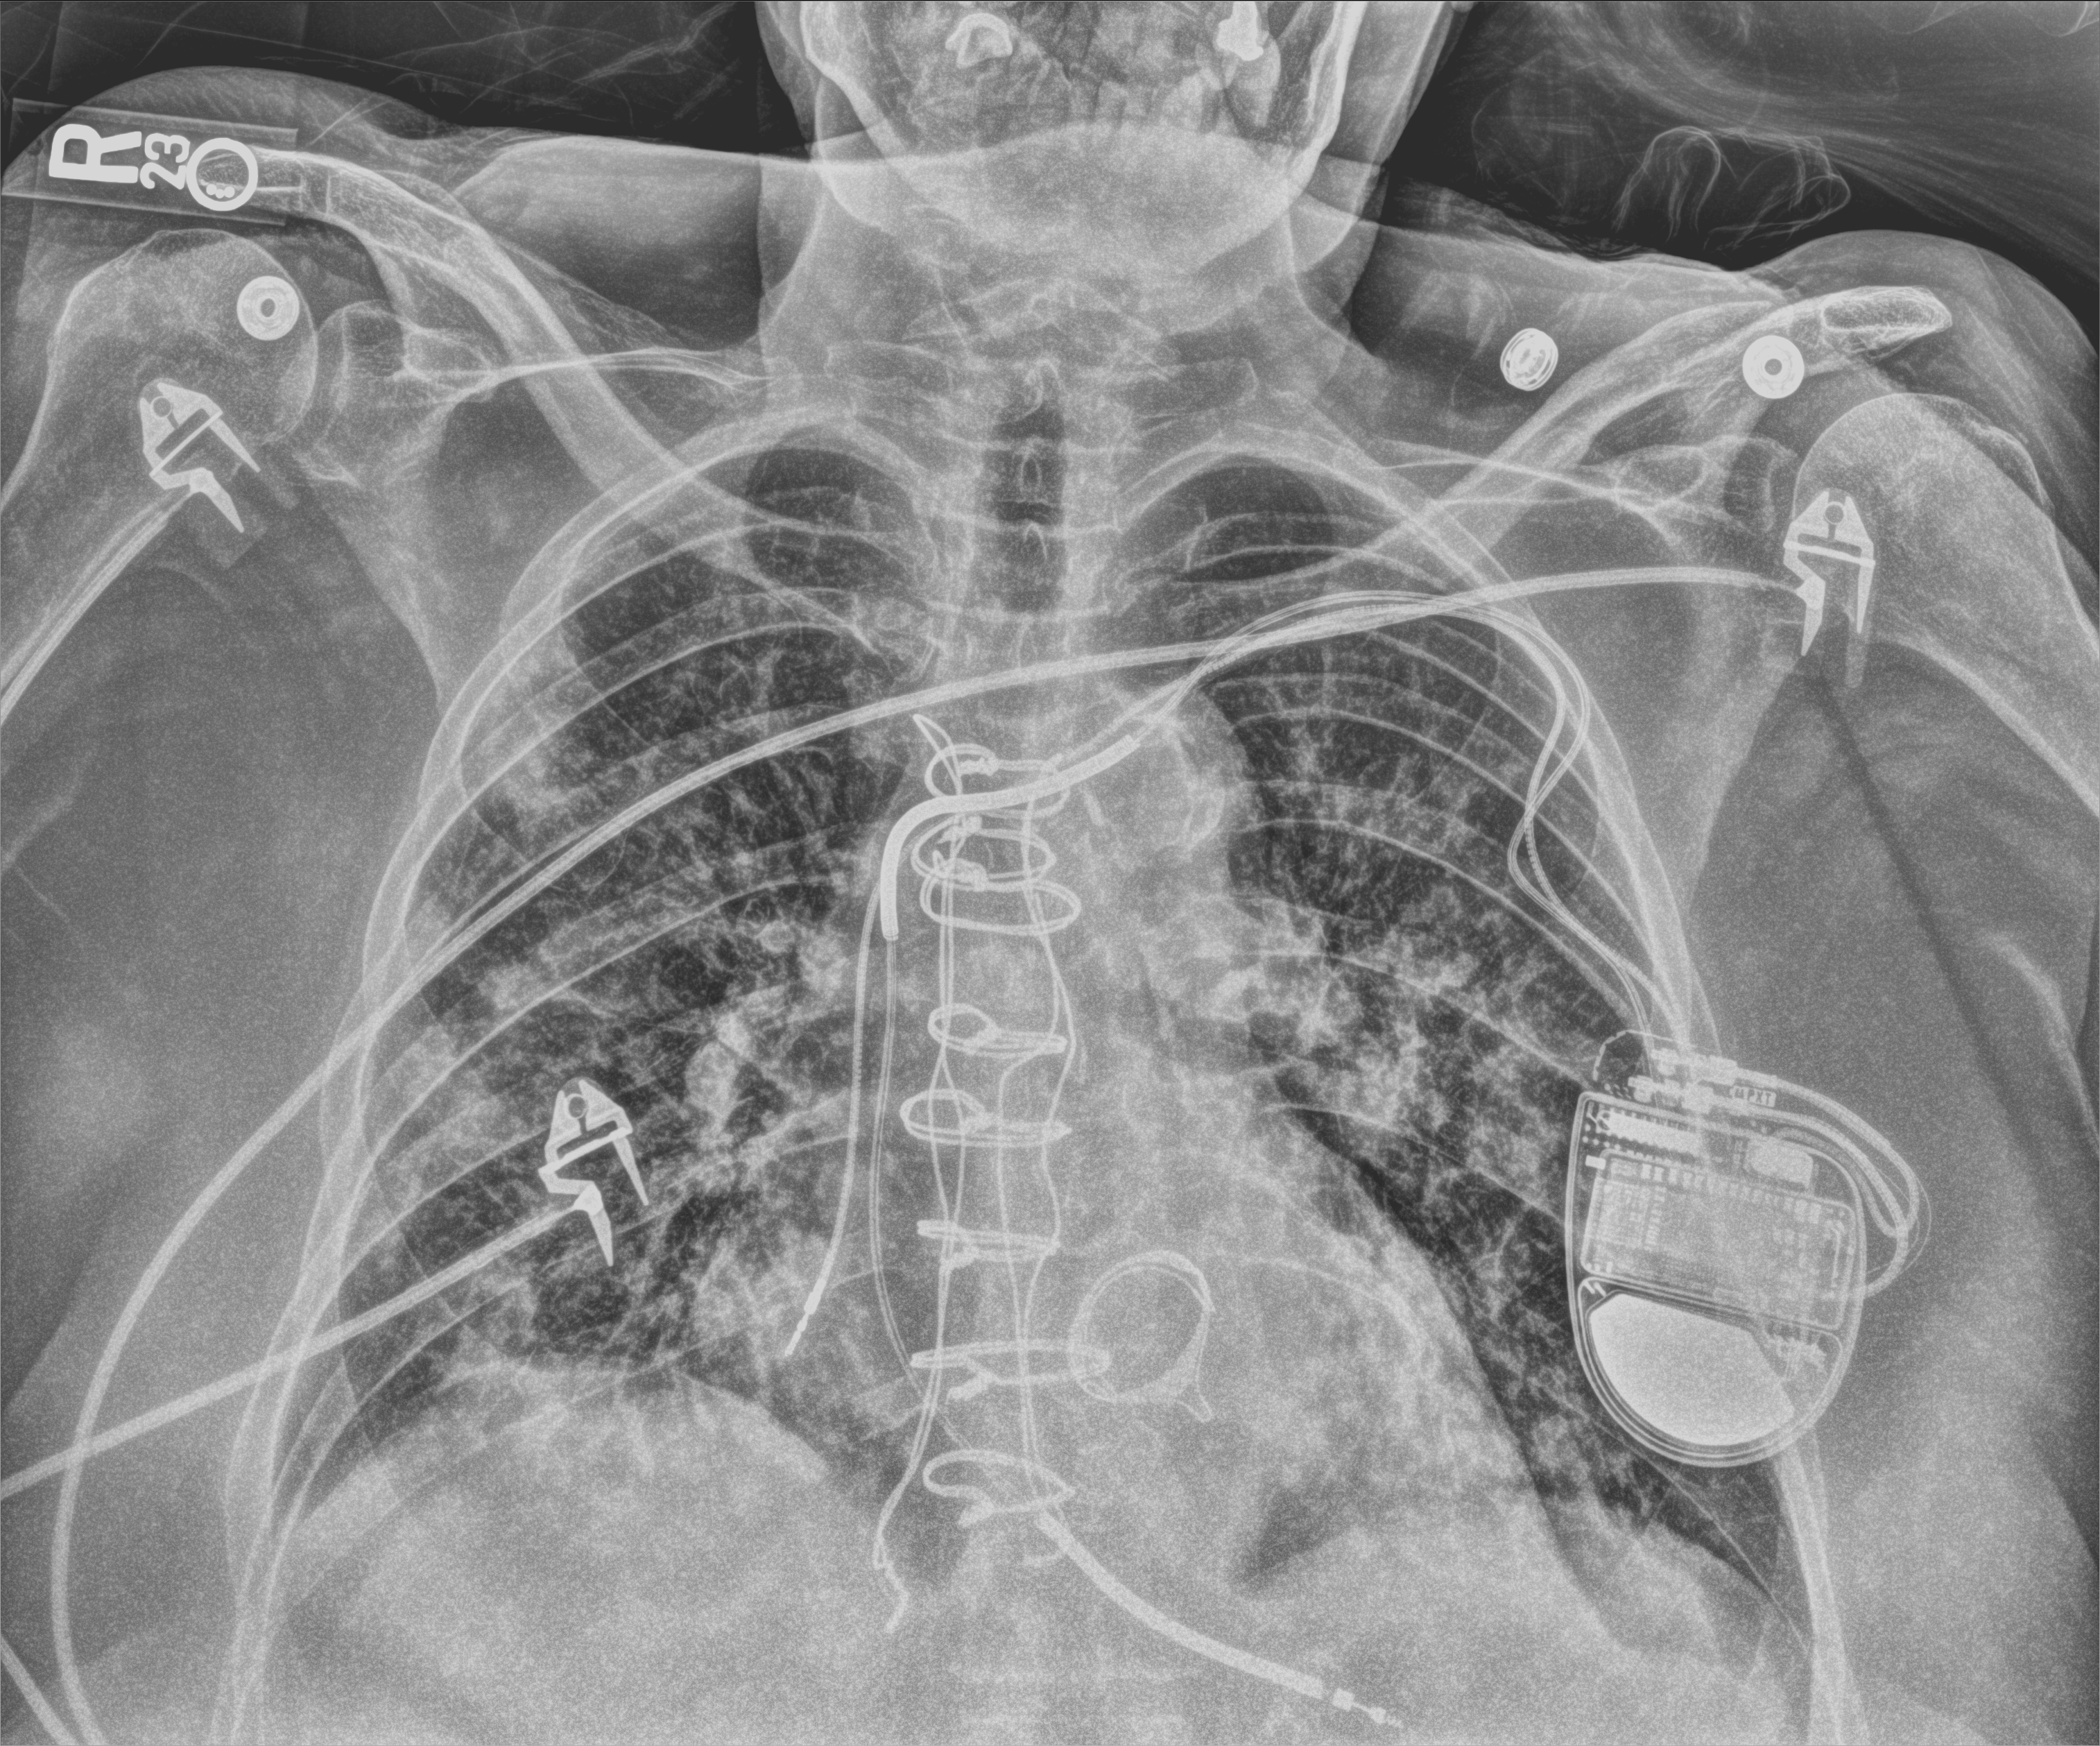
Bedside chest radiograph (computed radiography); anteroposterior (AP) projection. Female patient hospitalised with COVID-19, age 60–74 years.
From the hospital-stay record, not from the radiograph (when in the stay this image was taken is not recorded):
- admitted to intensive care during this hospital stay: yes
- length of hospital stay: 14 days
- mechanically ventilated during this hospital stay: no